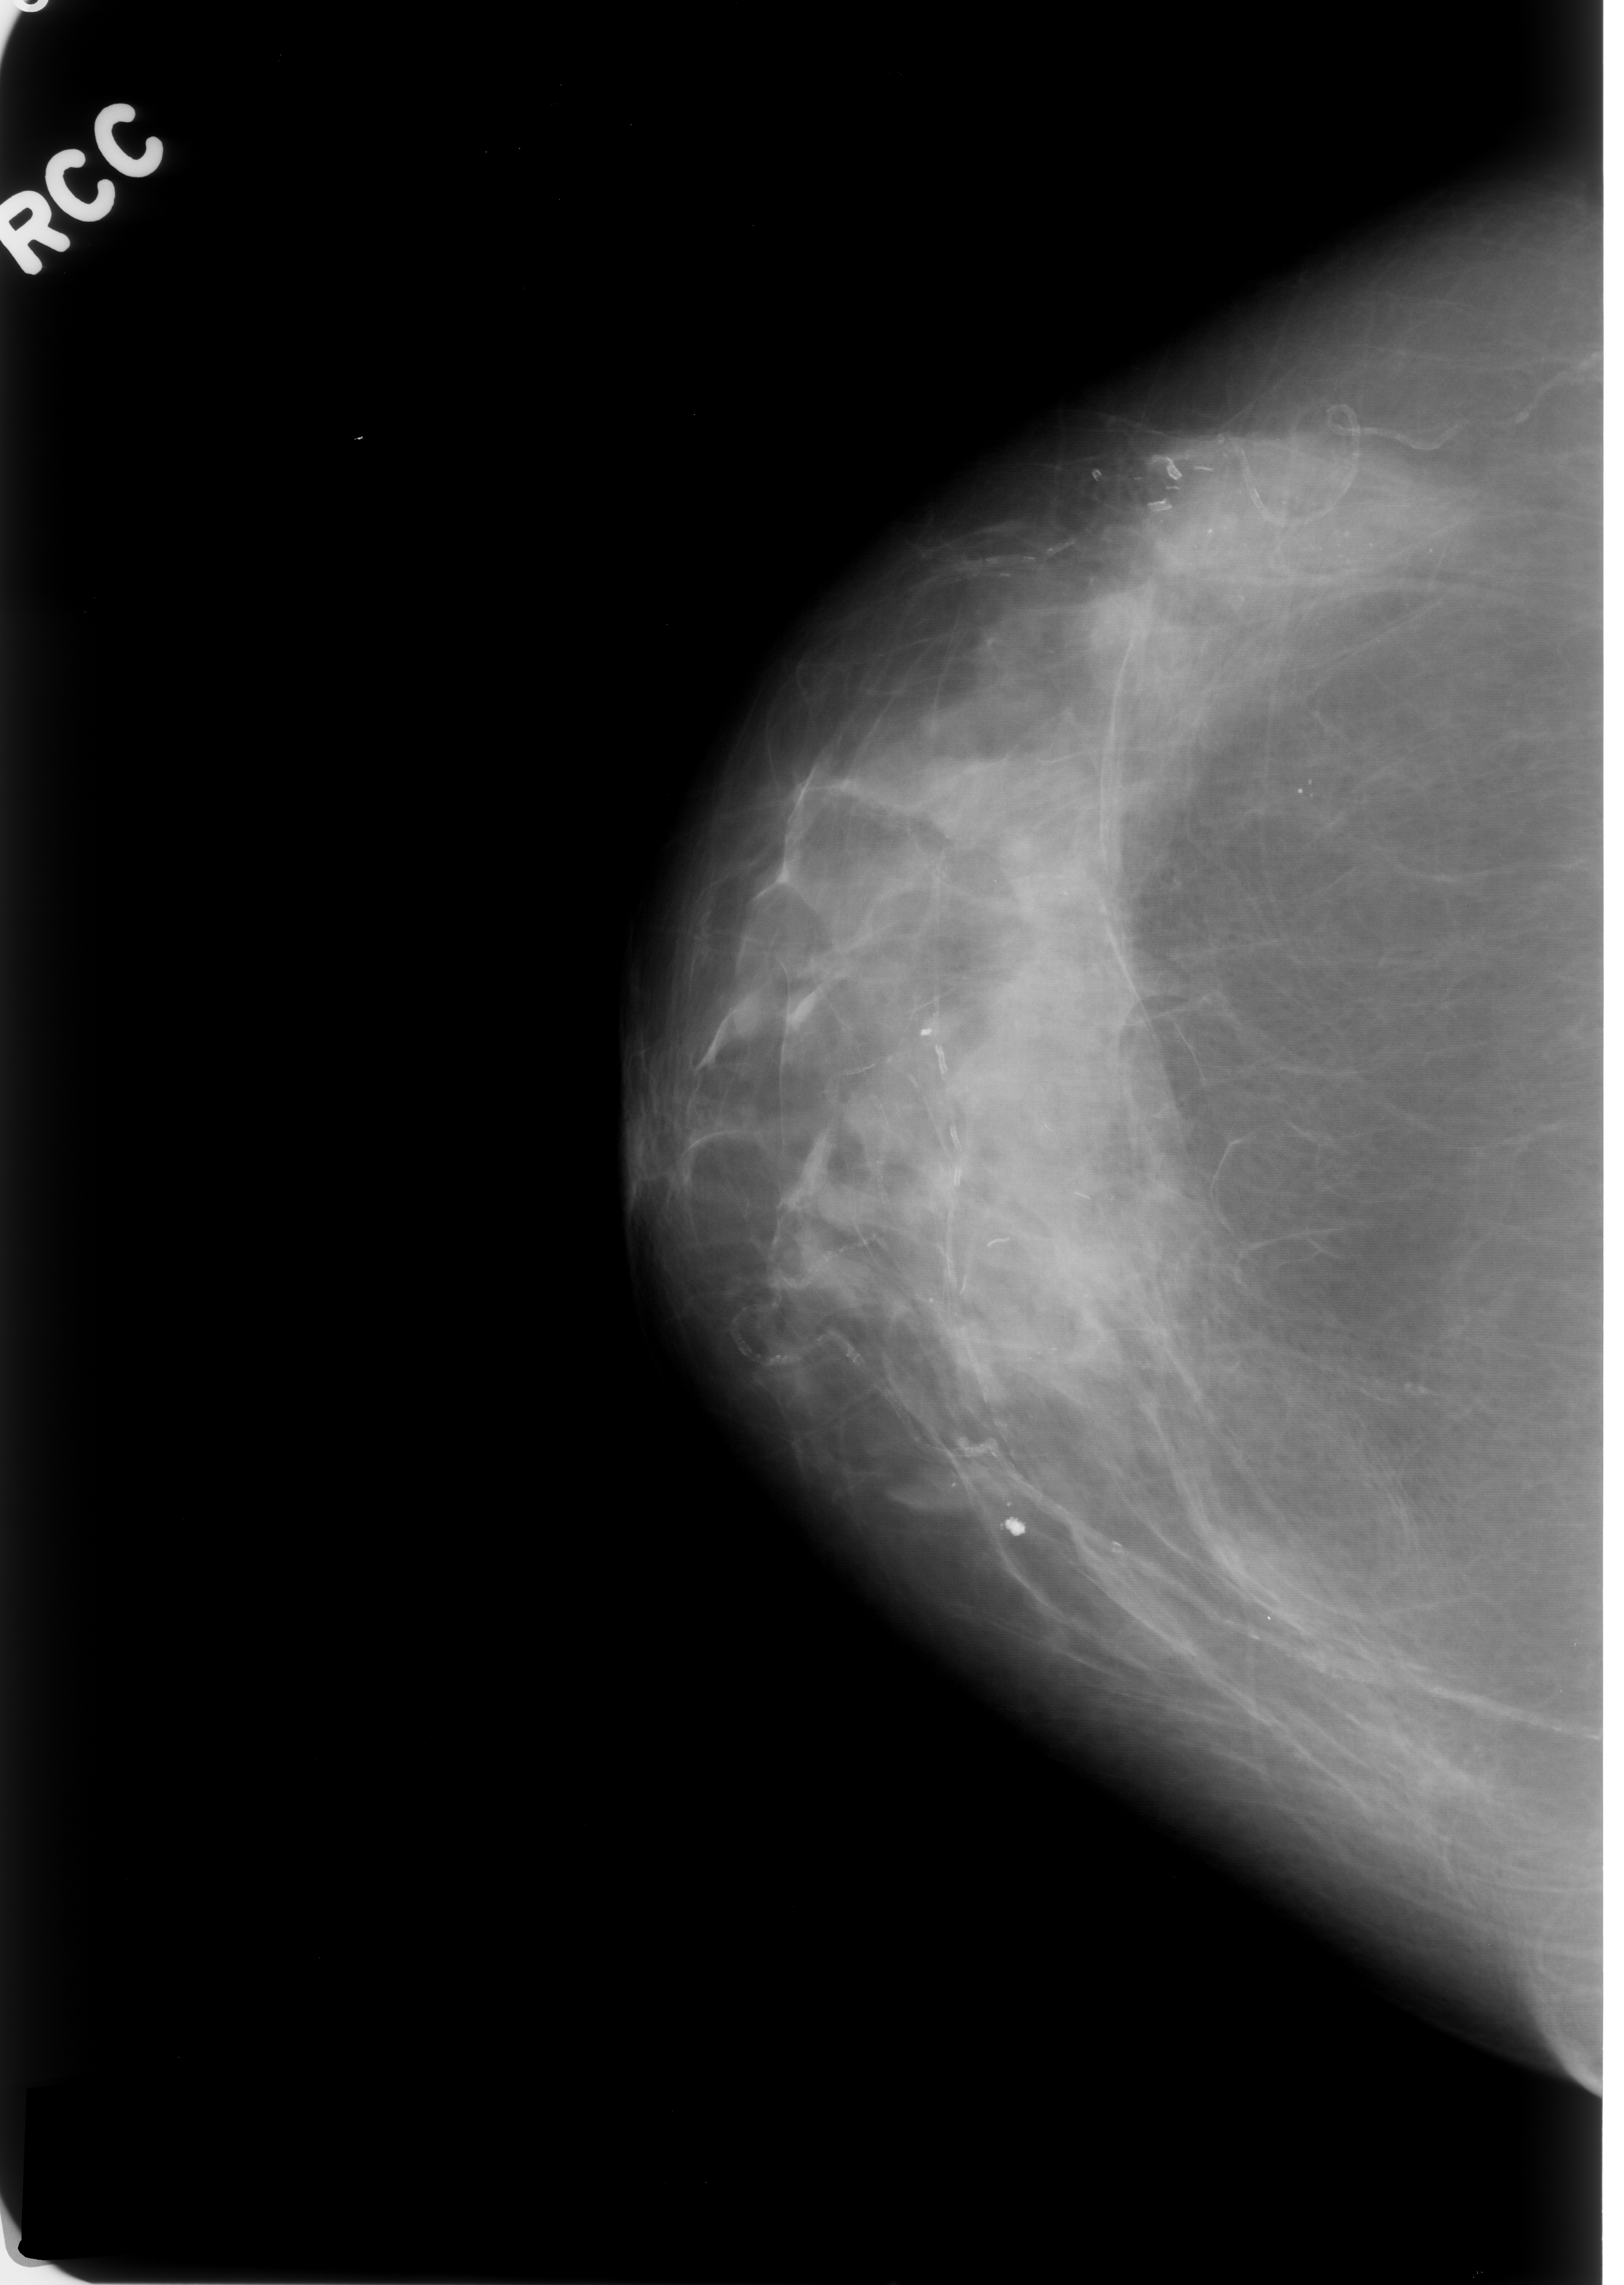
Mammogram (digitized film), right breast, craniocaudal (CC) view, BI-RADS breast density category 2 (scale 1–4).
Calcifications, morphology punctate, distribution segmental; BI-RADS assessment category 4; pathology (as recorded): benign.